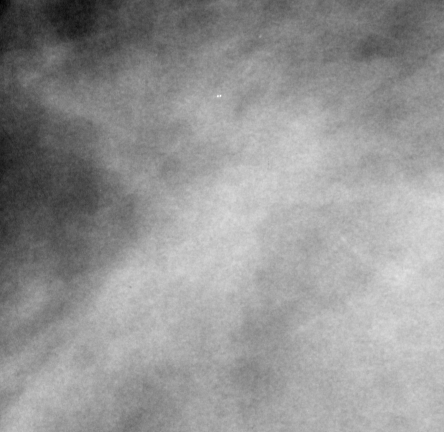
Crop from a digitized film mammogram around one marked abnormality; left breast; CC view; BI-RADS breast density category 3 (scale 1–4).
Mass, shape architectural distortion, margins spiculated; BI-RADS assessment category 5; subtlety rating 2 on a 1 (subtle) to 5 (obvious) scale; pathology result (as recorded, not read from the image): malignant.